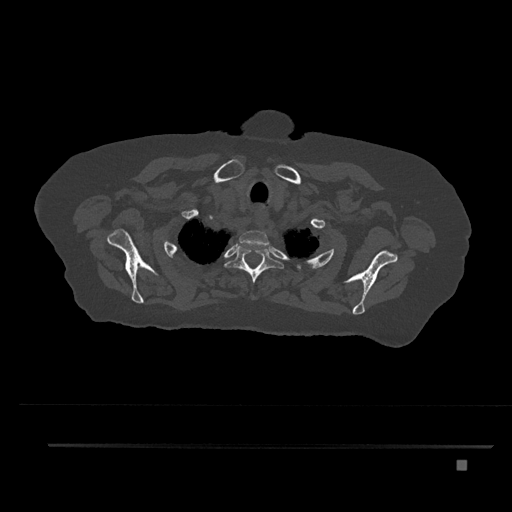
CT including the spine, one axial slice. Slice 675 of 797 in the series (ordered by position). Reconstruction kernel Br40s/3. 120 kVp. Bone window (W 1800 / L 400 HU). 0.5 mm slice thickness. 512 × 512 image matrix. Female patient, age 76 years. Case-level facts recorded for this patient, not image findings: primary cancer: lung; vertebrae with lytic lesions (as recorded): T11, L3.
Structures marked on this image (semi-automatically segmented with operator editing):
- T1 vertebra: bounding box (x1, y1, x2, y2) in pixels: (239, 230, 269, 247)
- T2 vertebra: (224, 244, 284, 298)